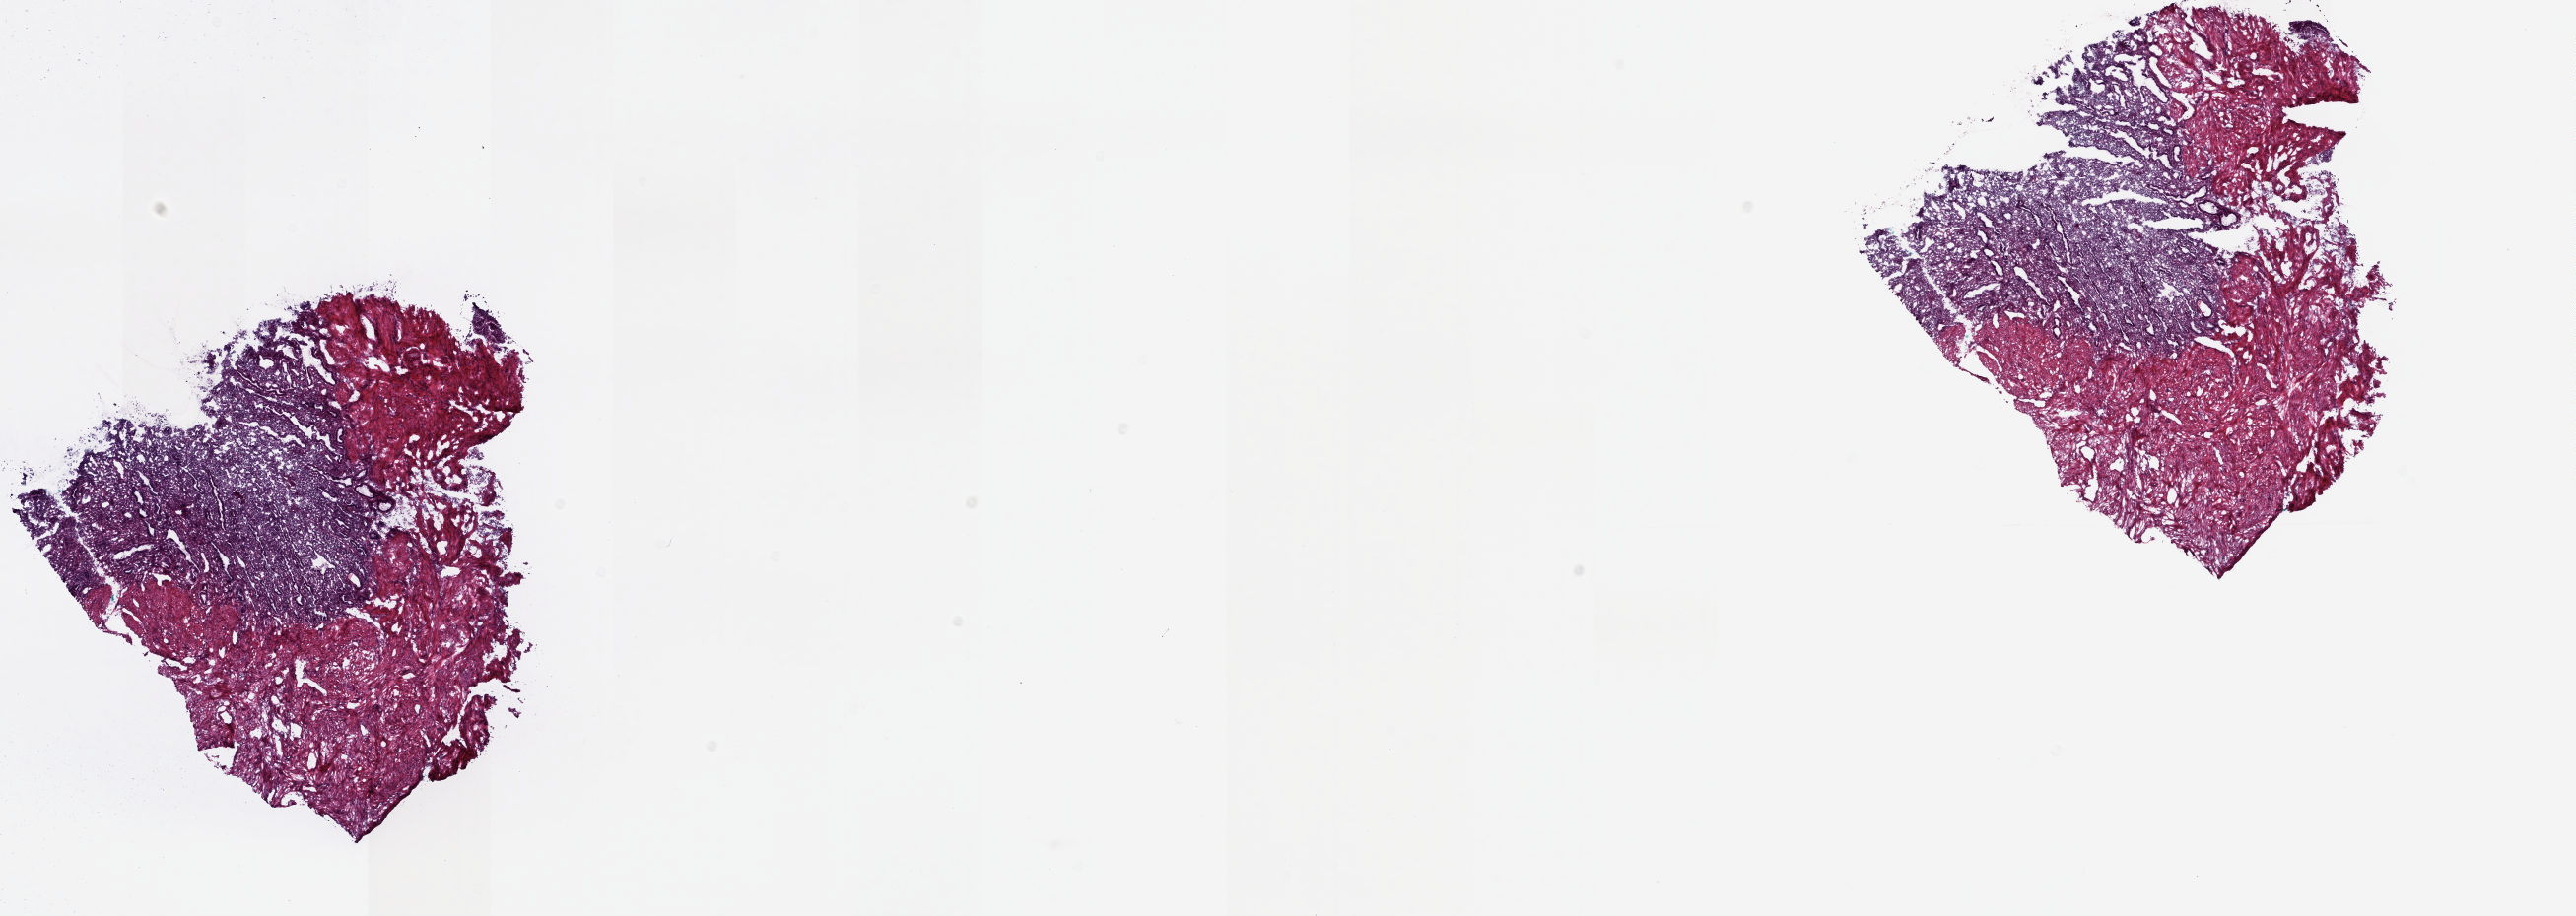
Hematoxylin and eosin (H&E) stained whole-slide image — shown as a low-resolution overview of the whole scanned area (about 20.8 x 7.4 mm, slide scanned at 20x); frozen section from the top of the tissue portion; sample: solid tissue normal (non-tumour tissue), uterus. Slide review estimates, as recorded: tumour cells 0%, normal cells 100%.
This section: solid tissue normal sample (biorepository sample class).